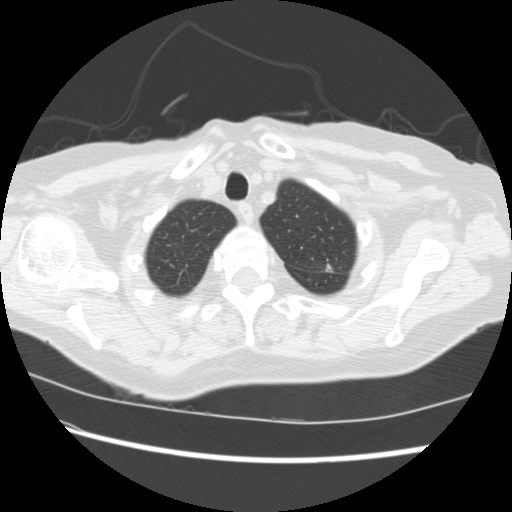
Axial slice from a low-dose chest CT screening exam; baseline annual screen; lung window (W 1500 / L -600 HU); 2.5 mm slice thickness; standard (soft-tissue) reconstruction kernel (STANDARD); slice 31 of 224 in the series. Female, age 74 years at enrolment. Former smoker at enrolment.
Lesion marked by an expert reader, bounding box (x1, y1, x2, y2) in pixels: (297, 250, 348, 286). The screening reader recorded 2 non-calcified nodules or masses ≥4 mm on this exam (left upper lobe, right lower lobe); which of them this box marks is not recorded. Official screen result: positive, change unspecified: nodule(s) >= 4 mm or enlarging nodule(s), mass(es), or other non-specific abnormalities suspicious for lung cancer. Lung cancer was diagnosed 309 days after this screen: non-small cell carcinoma, left upper lobe, stage IV (AJCC 6th edition).